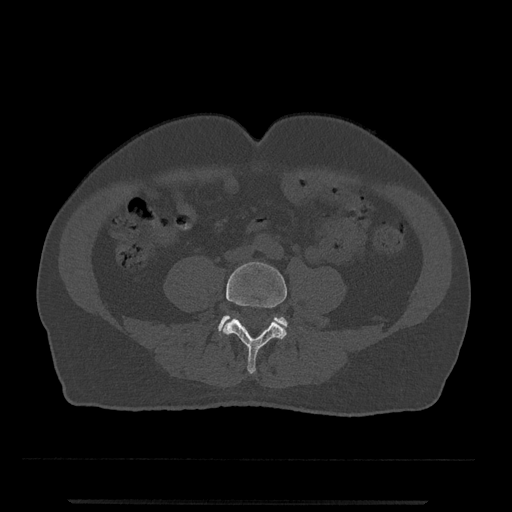
CT including the spine, one axial slice; slice 120 of 797 in the series (ordered by position); reconstruction kernel Br40s/3; bone window (W 1800 / L 400 HU); 0.5 mm slice thickness; 512 × 512 image matrix, field of view 419 × 419 mm. Male patient, age 63 years. Case-level facts recorded for this patient, not image findings: primary cancer: prostate.
Outlined on this slice (semi-automatic segmentation, software-assisted and operator-edited):
- L4 vertebra: box from (x=222, y=262) to (x=287, y=374) px
- L5 vertebra: (x=218, y=315)–(x=288, y=332)